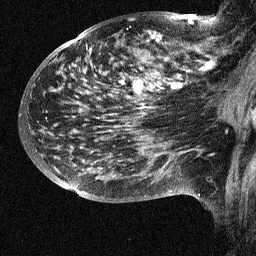
Breast MRI (dynamic contrast-enhanced), one sagittal slice; dynamic contrast-enhanced study with each time point stored as its own series, time point 2 of 3 at this slice position (early post-contrast, ordered by acquisition time); 1.5 T; TE 4.5 ms, TR 11 ms; 256 × 256 image matrix, field of view 200 × 200 mm. Patient: female, 38 years. Case-level facts recorded for this patient, not image findings: setting: breast cancer imaged before/during neoadjuvant chemotherapy; receptor status: HR-positive, HER2-negative.
Annotated regions visible in this slice (semi-automatic segmentation, software-assisted and operator-edited):
- analysis volume of interest (the breast-tissue region the enhancement analysis was run in; not a lesion): bounding box <88,18,252,126> (left, top, right, bottom; pixels)
- tumour enhancement mask (voxels above the 90 % enhancement threshold inside the analysis volume of interest): <120,19,211,107>